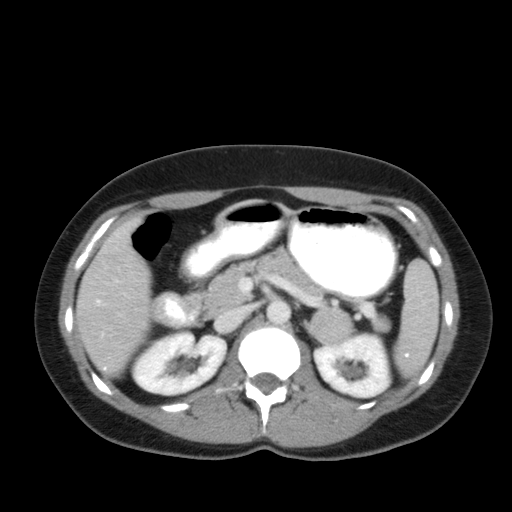
Contrast-enhanced abdominal CT, one axial slice. Slice 30 of 92 in the series (ordered by position). 120 kVp. Intravenous contrast given. Soft-tissue window (W 400 / L 40 HU). 5 mm slice thickness. 512 × 512 image matrix, field of view 369 × 369 mm. Patient: female, 35 years. From the clinical record (not read from this slice): diagnosis: adrenocortical carcinoma; tumour side: left adrenal; tumour size at pathology: 6.6 cm; Ki-67 index: 5 %; stage (as recorded): 2.
Structures marked on this image (semi-automatic segmentation, software-assisted and operator-edited):
- mass: bounding box <311,308,352,342> (left, top, right, bottom; pixels)